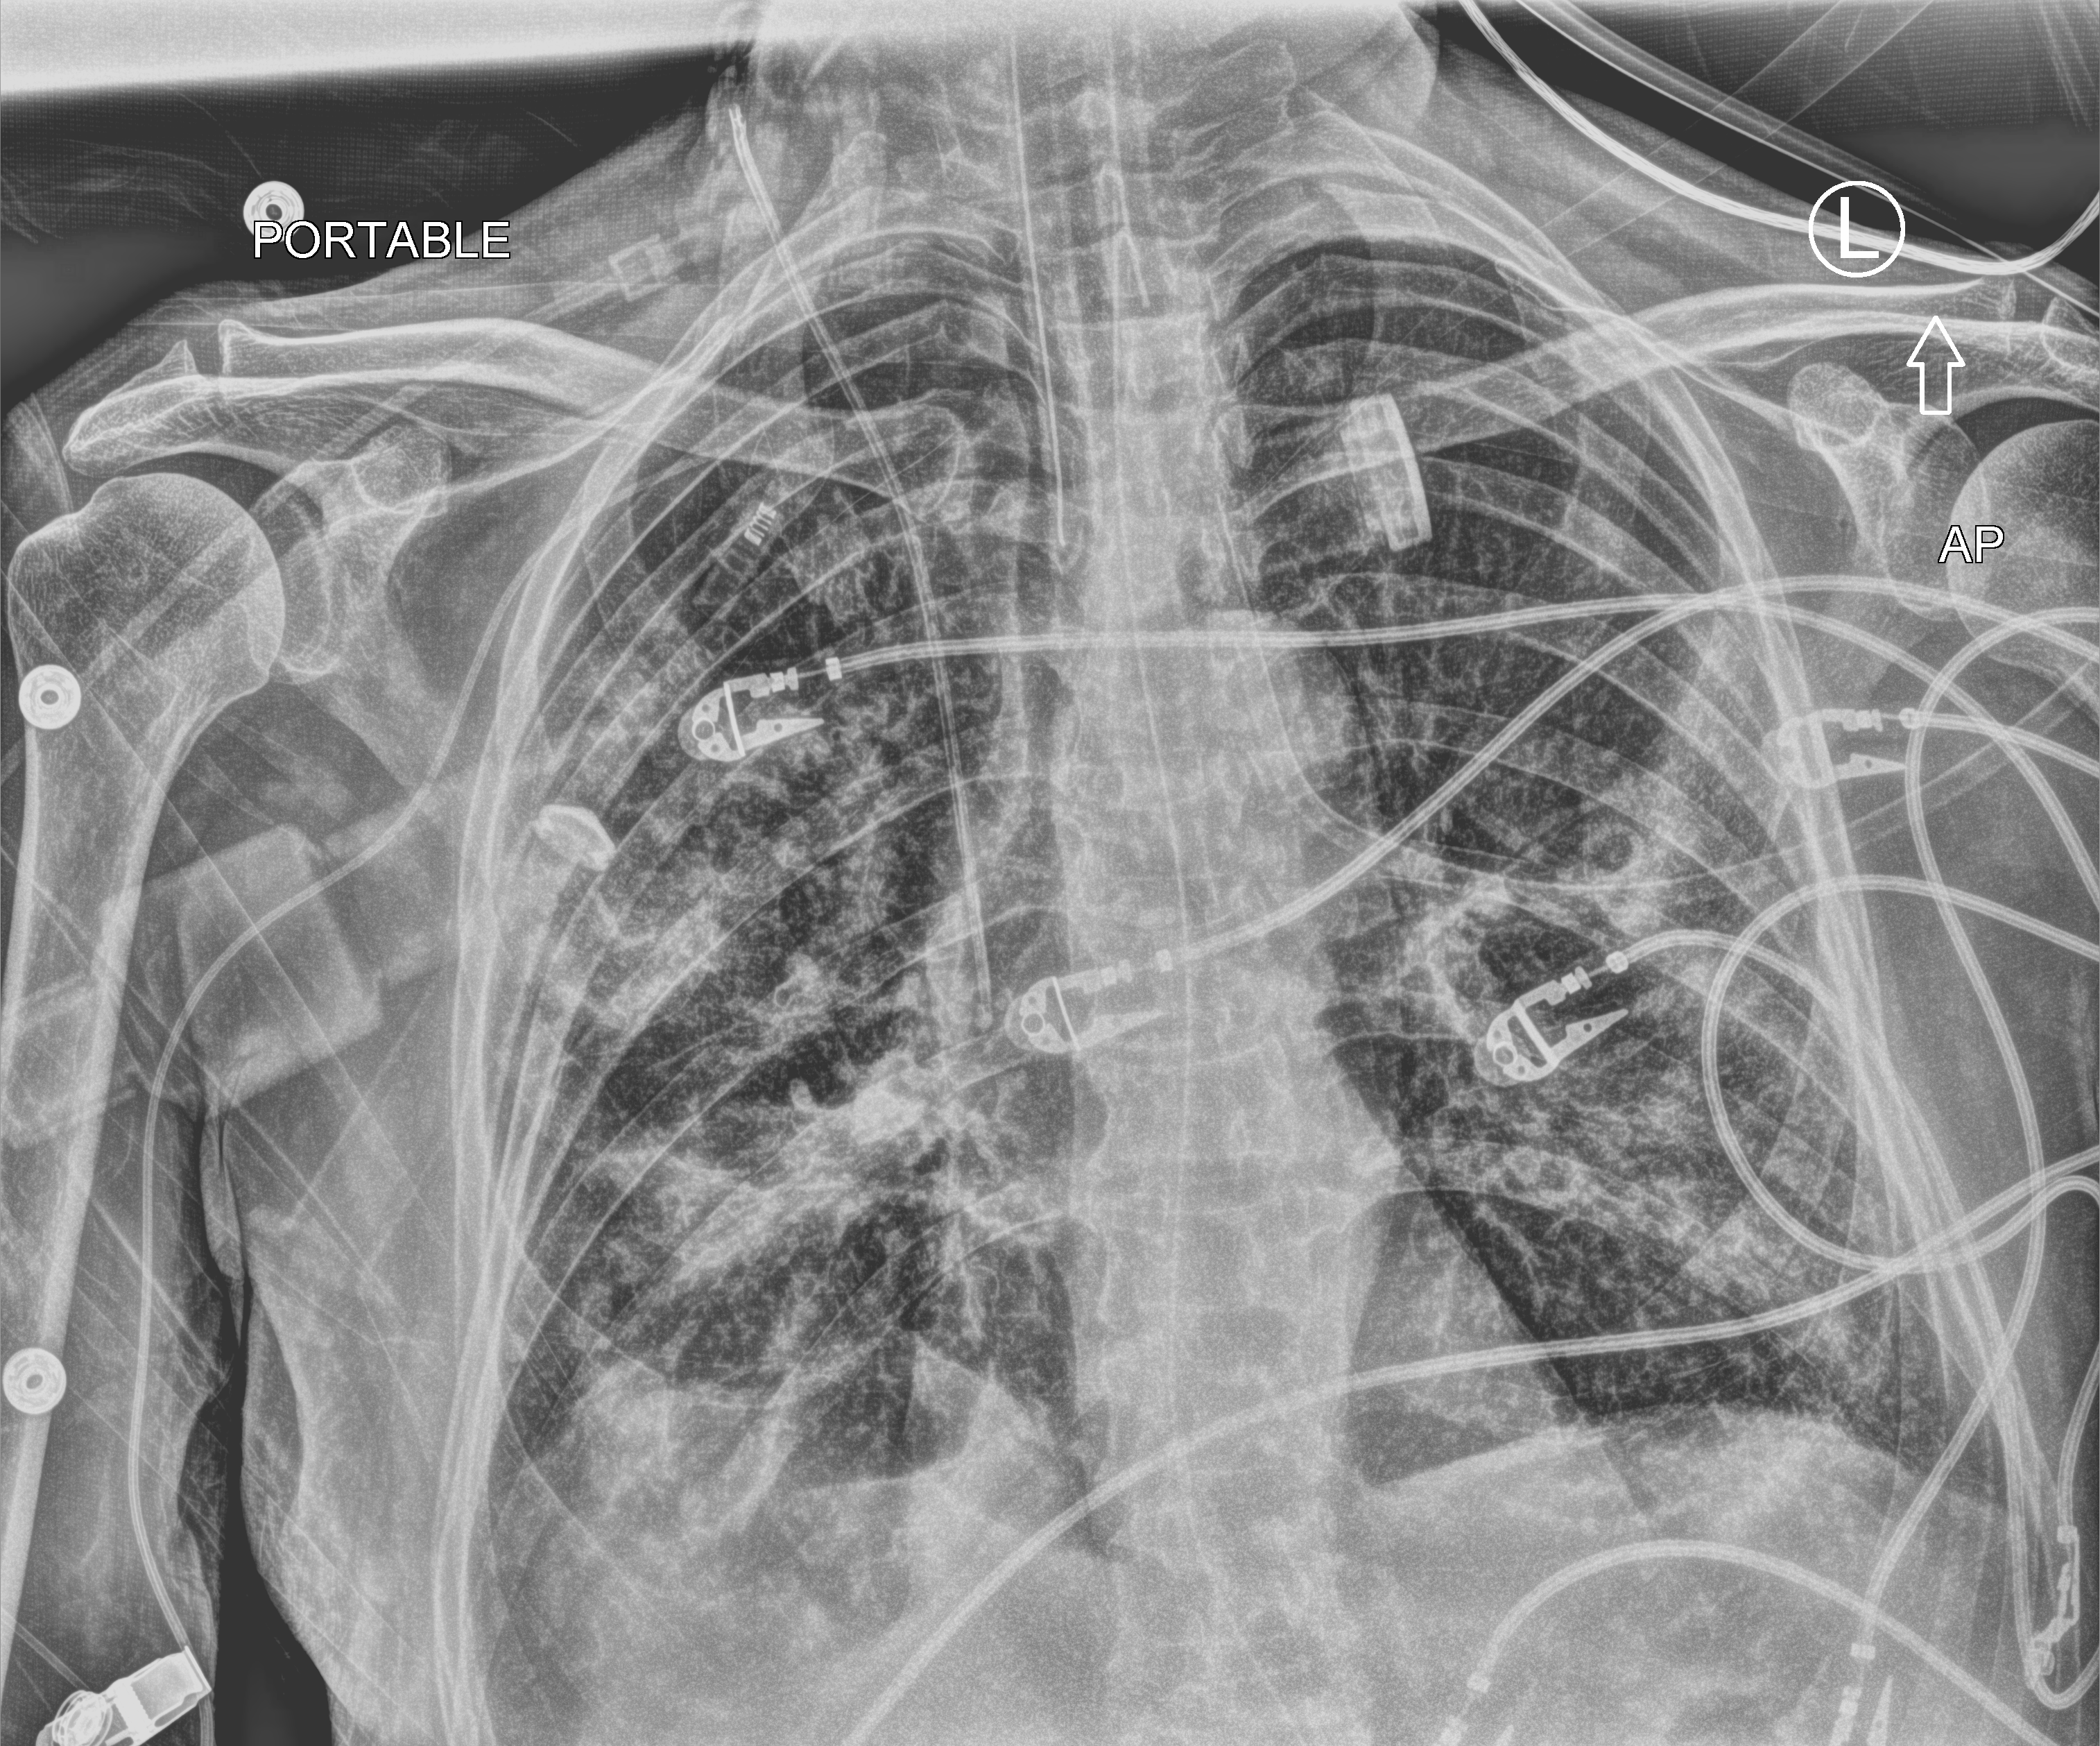
Portable chest radiograph; anteroposterior (AP) projection. Male patient hospitalised with COVID-19, age 75–90 years.
Hospital-stay facts (about this admission, not read from this image; timing relative to this image not recorded): mechanically ventilated during this hospital stay: yes.